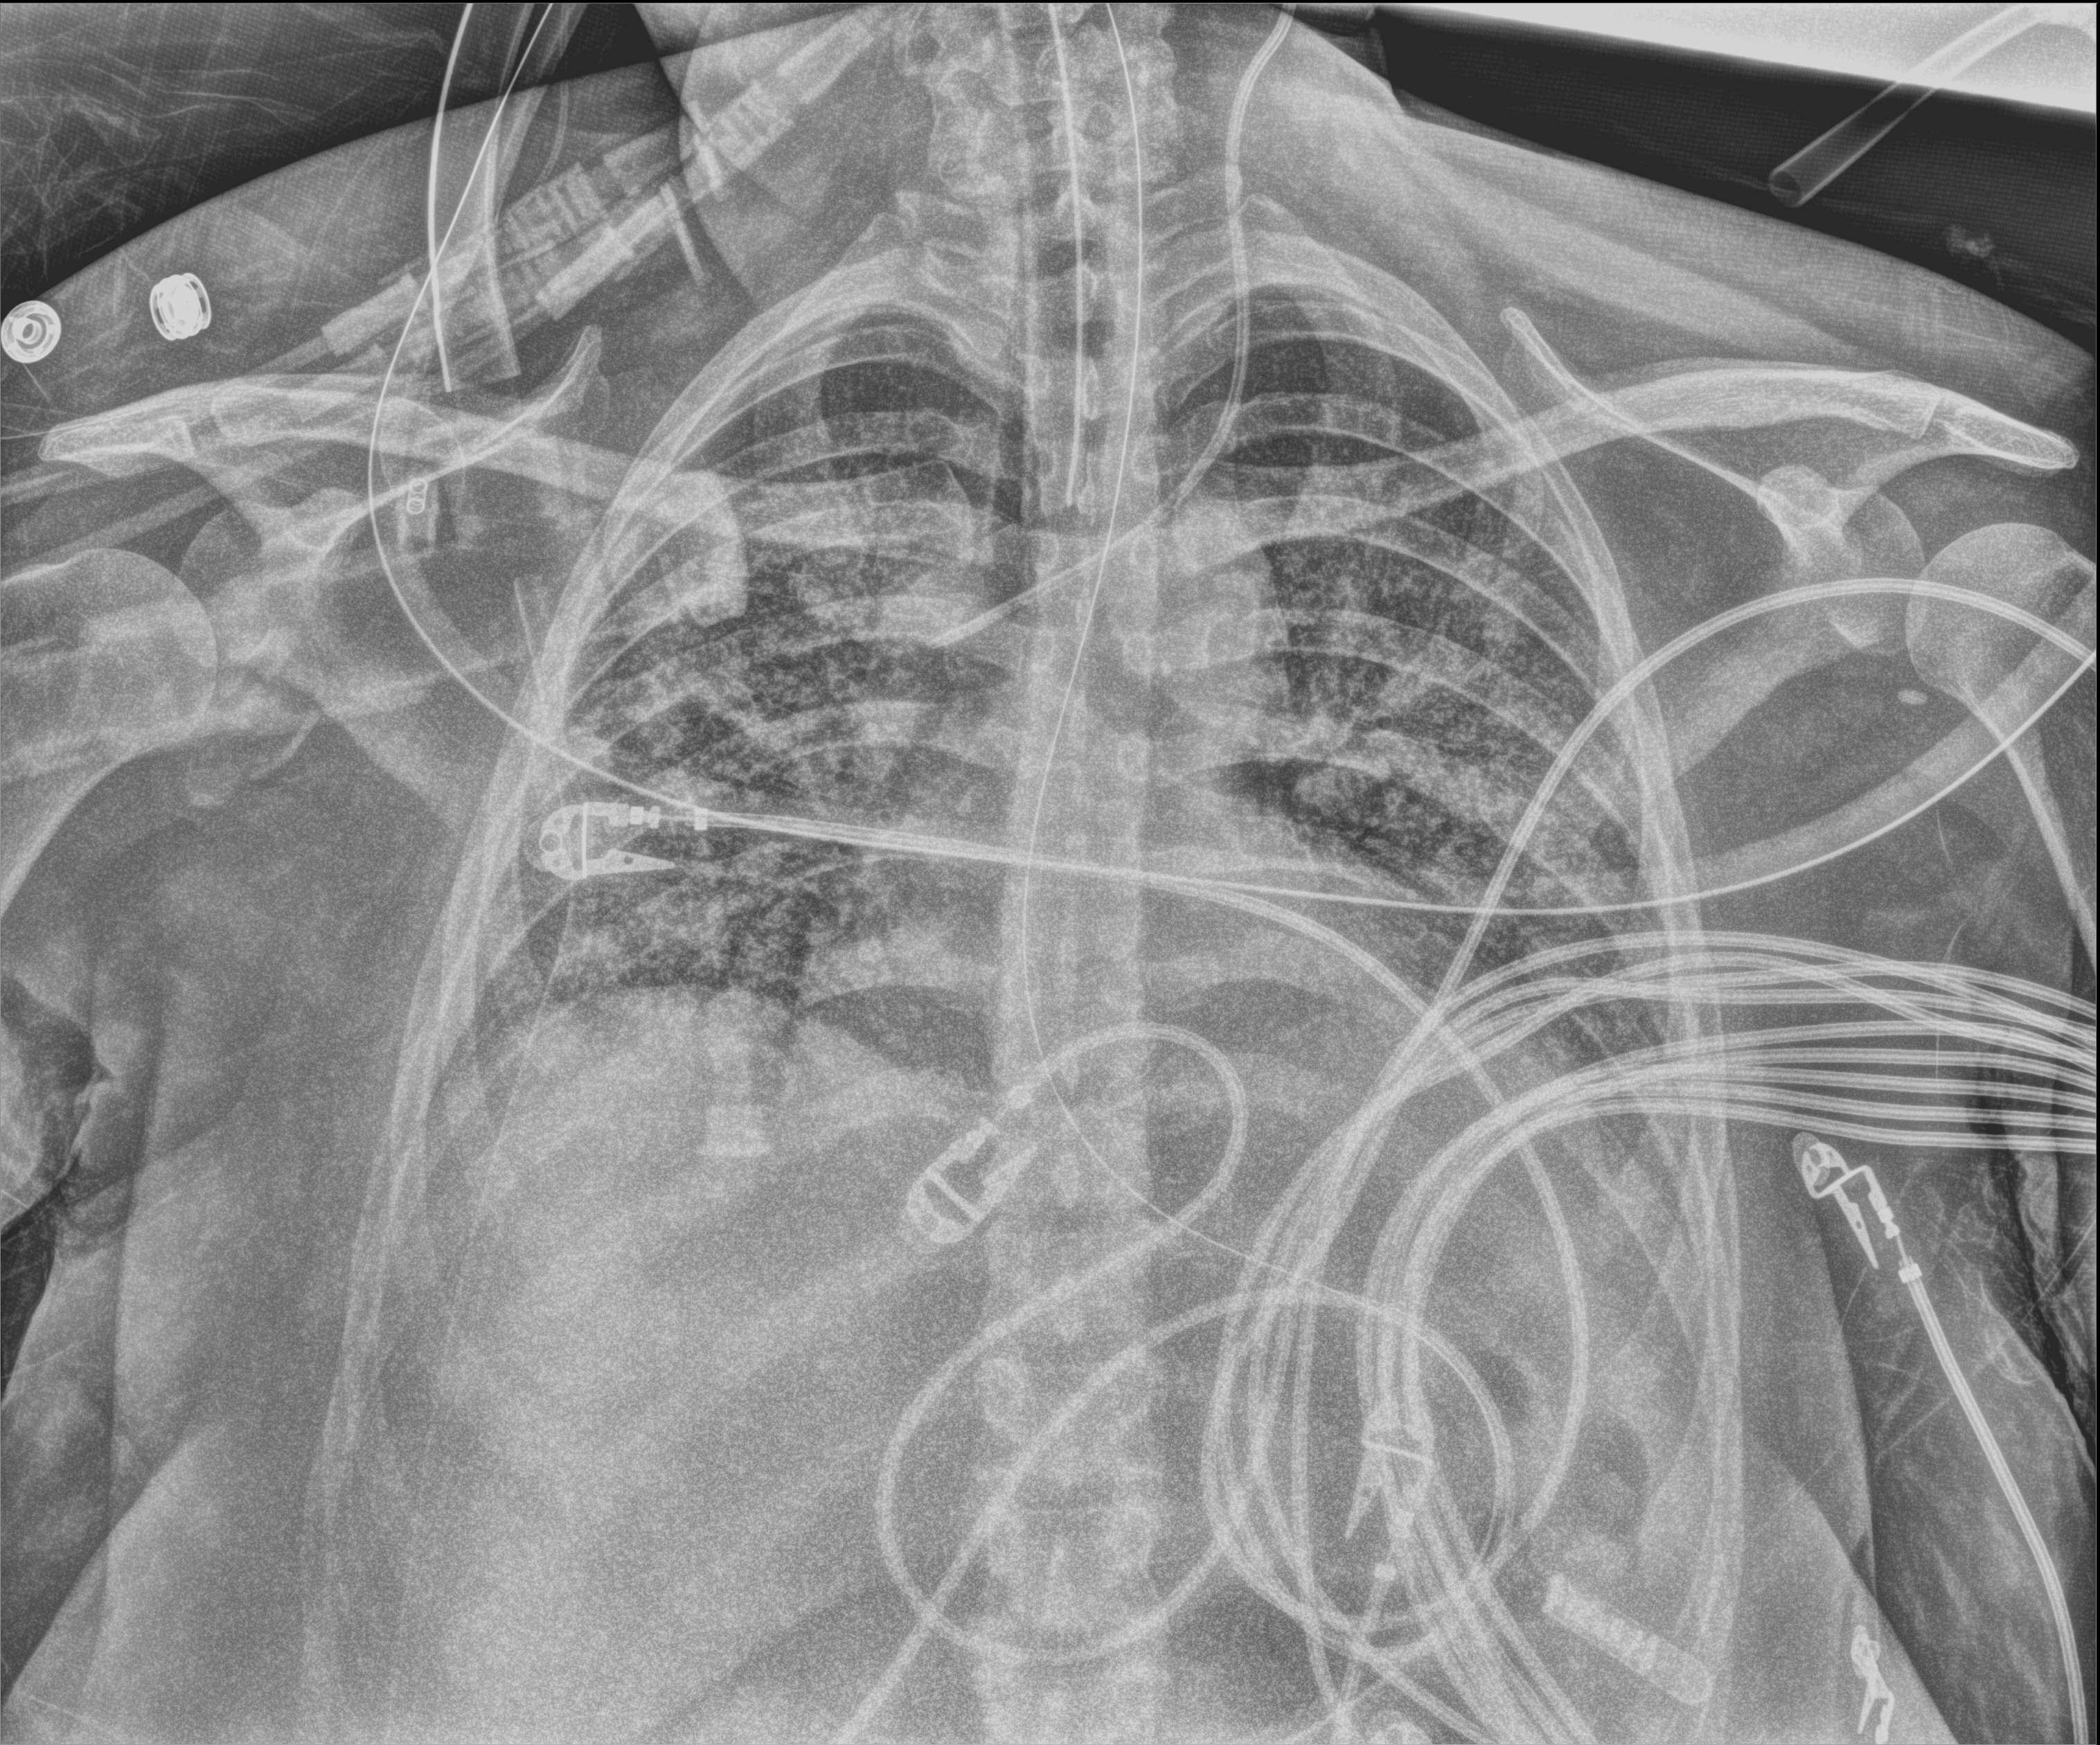
Portable chest radiograph; anteroposterior (AP) projection. Female patient hospitalised with COVID-19, age 18–59 years.
Hospital-stay facts (about this admission, not read from this image; timing relative to this image not recorded): admitted to intensive care during this hospital stay: no; length of hospital stay: 33 days; mechanically ventilated during this hospital stay: yes.